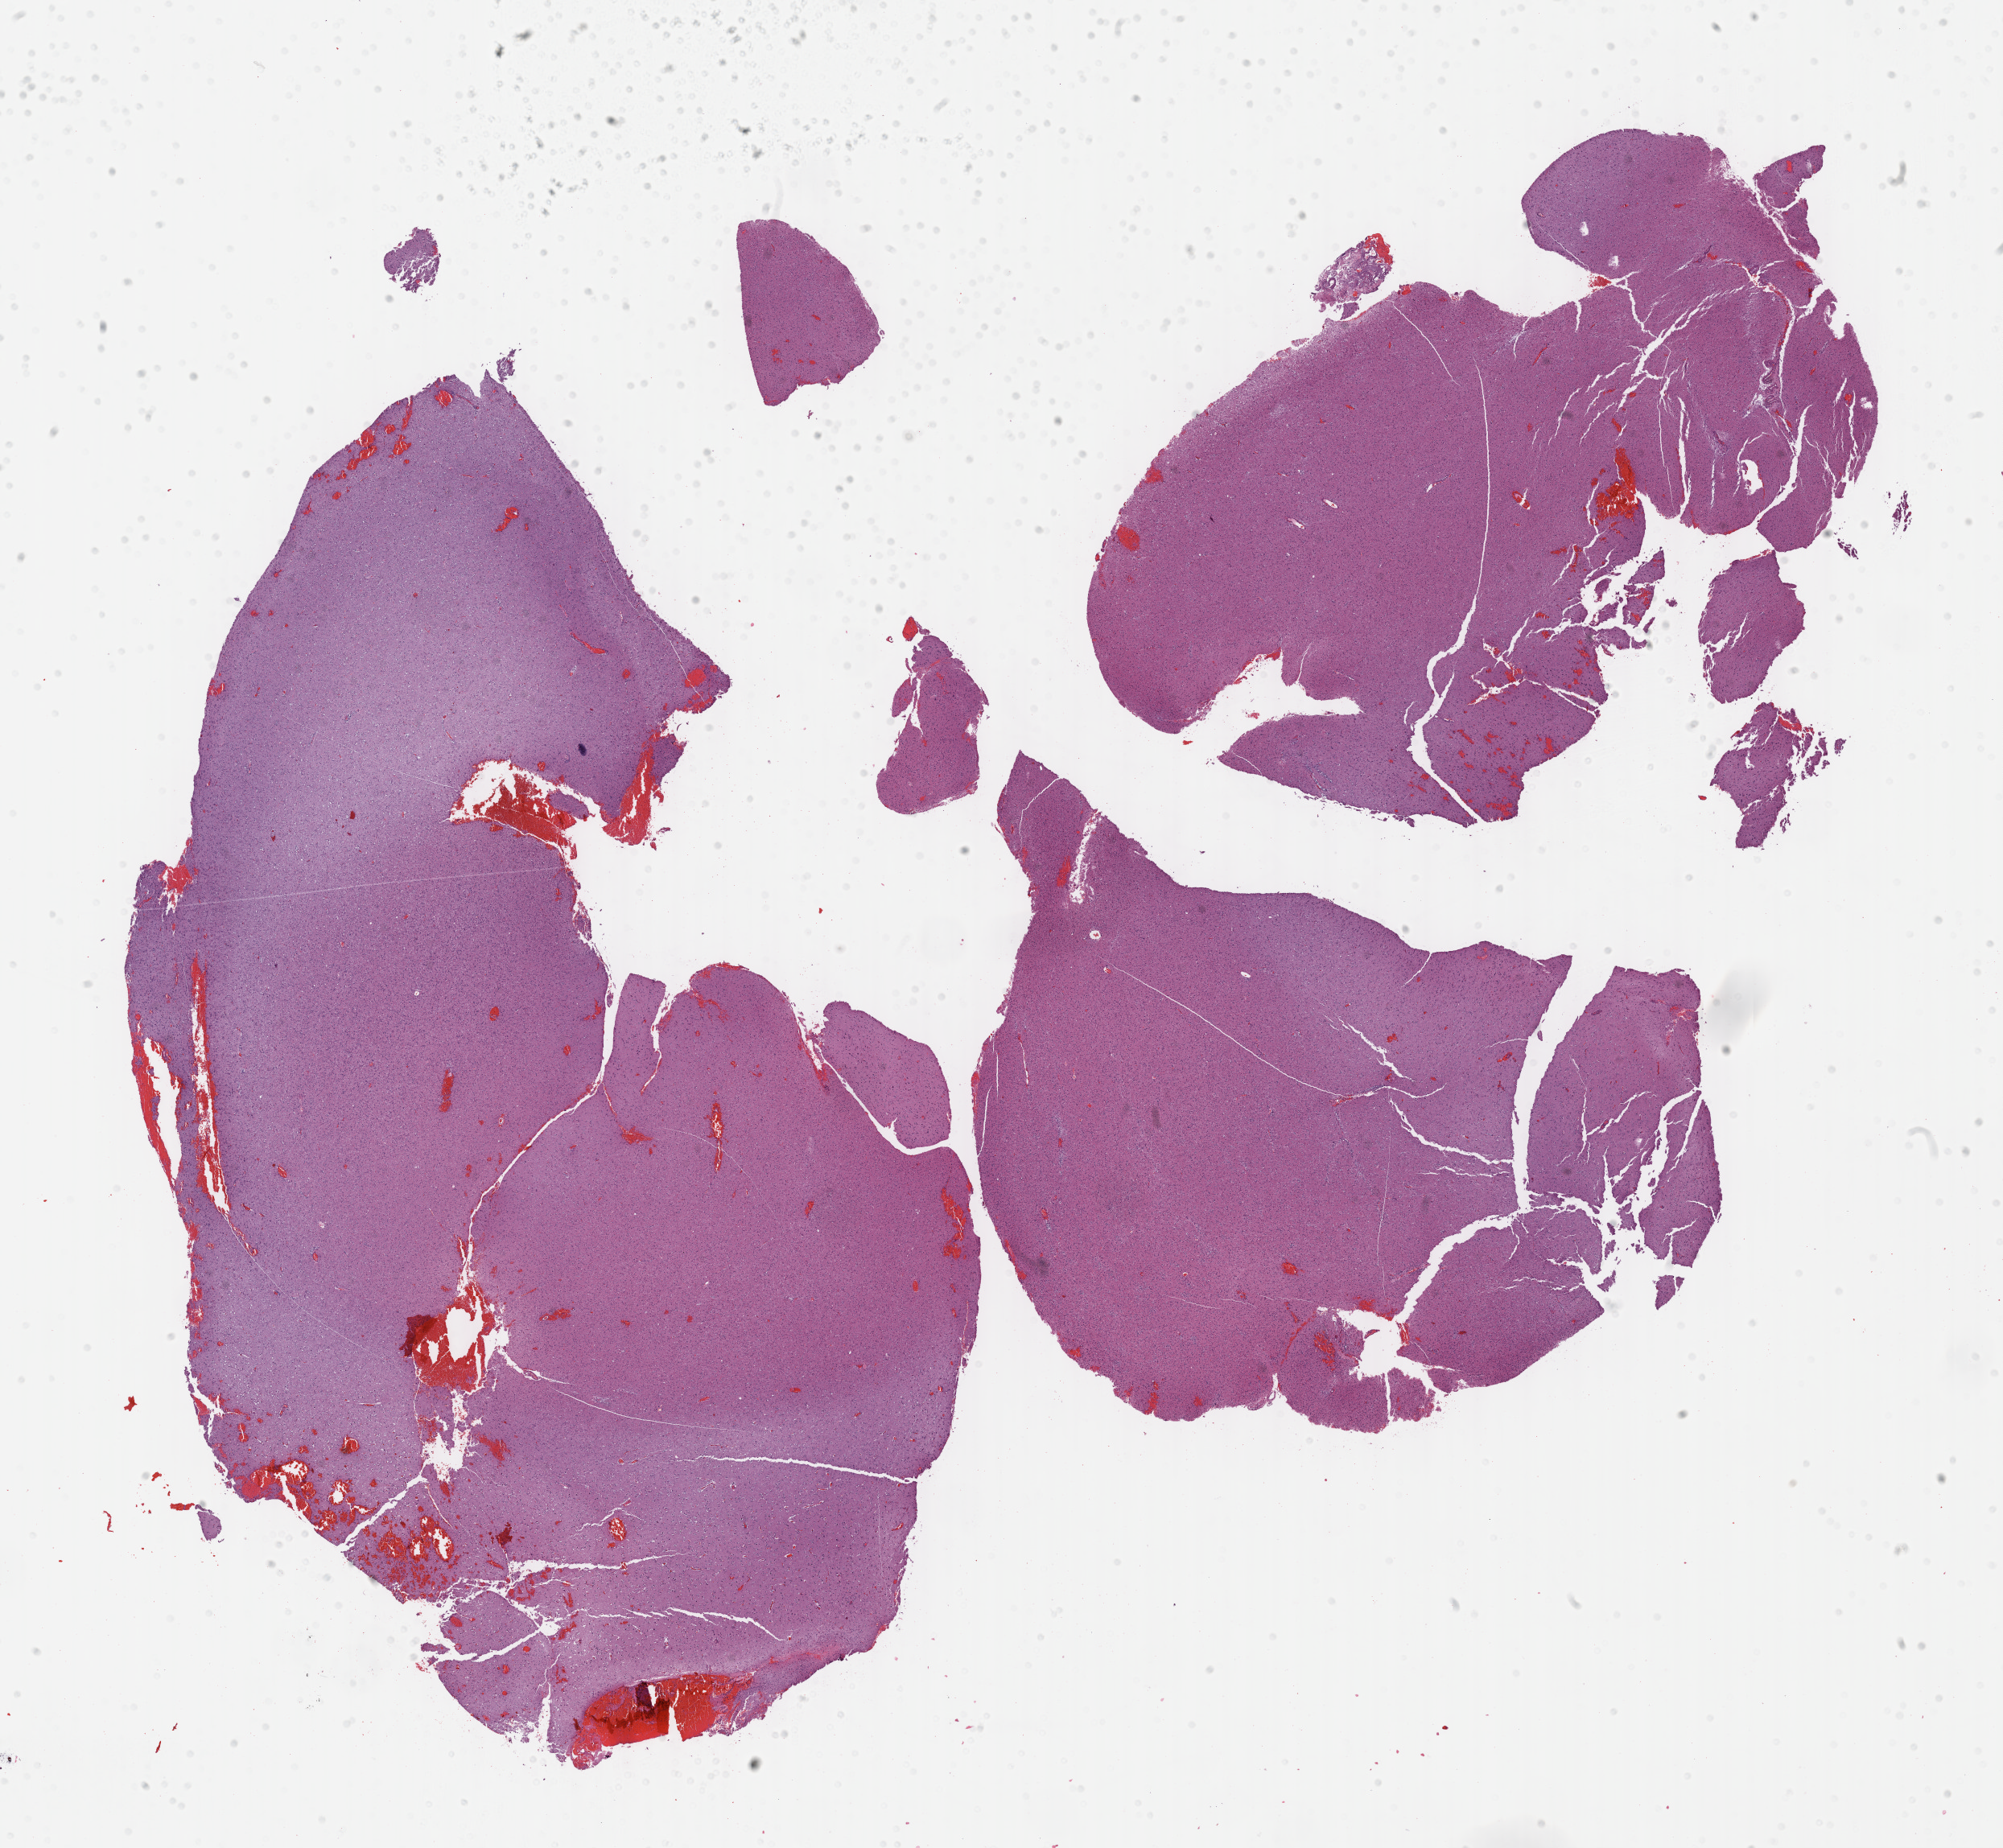
Digitized Hematoxylin and eosin (H&E) stained tissue section (whole slide), low-resolution overview of the scanned area, about 20.1 x 18.6 mm (from a 40x scan). FFPE section. Primary tumour sample from the brain. Male patient; age at initial diagnosis 28 years.
Pathologic diagnosis: Mixed glioma.